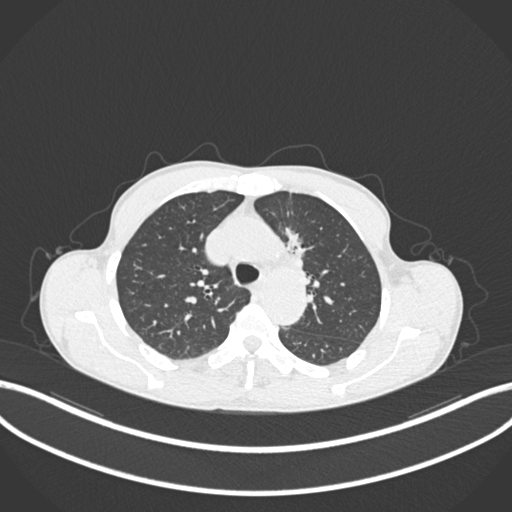
Chest CT, one axial slice. Reconstruction kernel B30f. Lung window (W 1500 / L -600 HU). 1 mm slice thickness. 512 × 512 image matrix, field of view 400 × 400 mm. Patient: male, 58 years. Case-level facts recorded for this patient, not image findings: clinical TNM (as recorded): T1c N1 M0.
Outlined on this slice (bounding box drawn by a radiologist):
- lung tumour (recorded histology: adenocarcinoma): bounding box <281,220,312,279> (left, top, right, bottom; pixels)